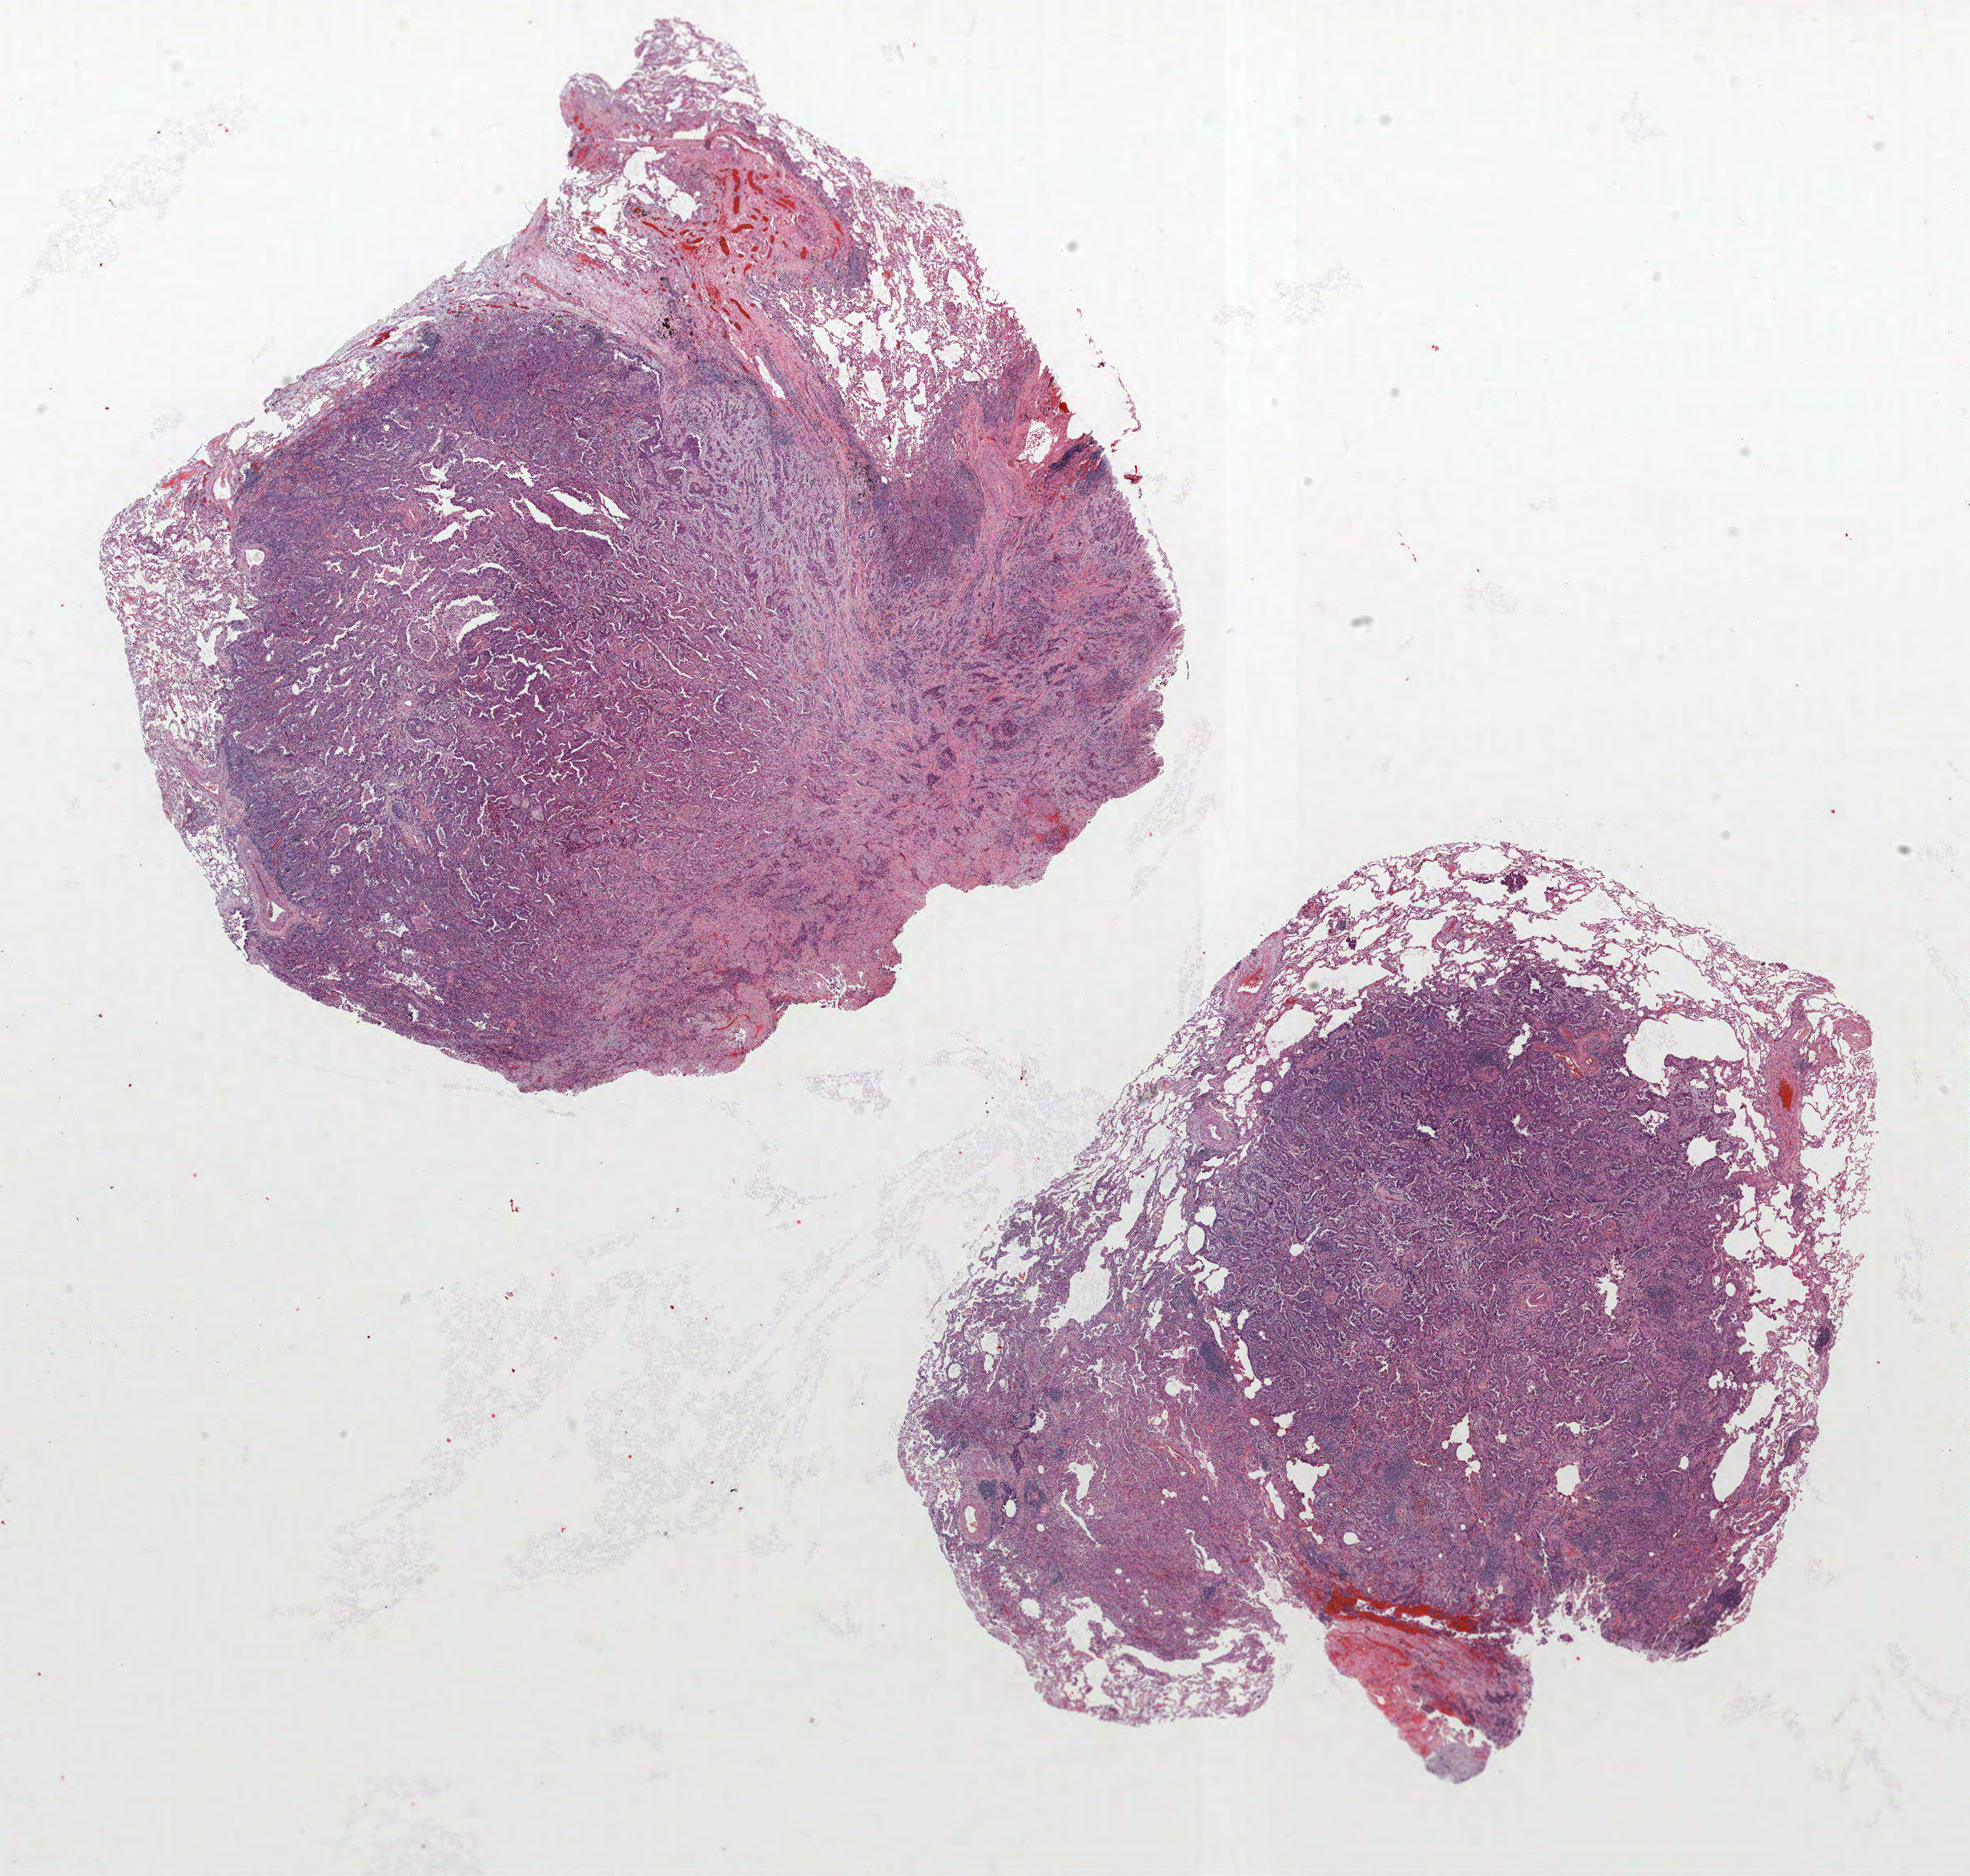
Hematoxylin and eosin (H&E) stained whole-slide image — whole scanned area (about 19.7 x 18.7 mm, slide scanned at 40x) shown as a low-resolution overview, formalin-fixed paraffin-embedded (FFPE) section, lung. Female patient, aged 72 at enrolment. Grade: moderately differentiated (G2).
Primary tumour location (clinical record): right upper lobe. Participant's lung-cancer diagnosis: Adenocarcinoma, NOS. Tumour size (pathology): 15 mm. ICD-O-3 topography: upper lobe of lung (C34.1). Stage (AJCC 6th edition): IA.